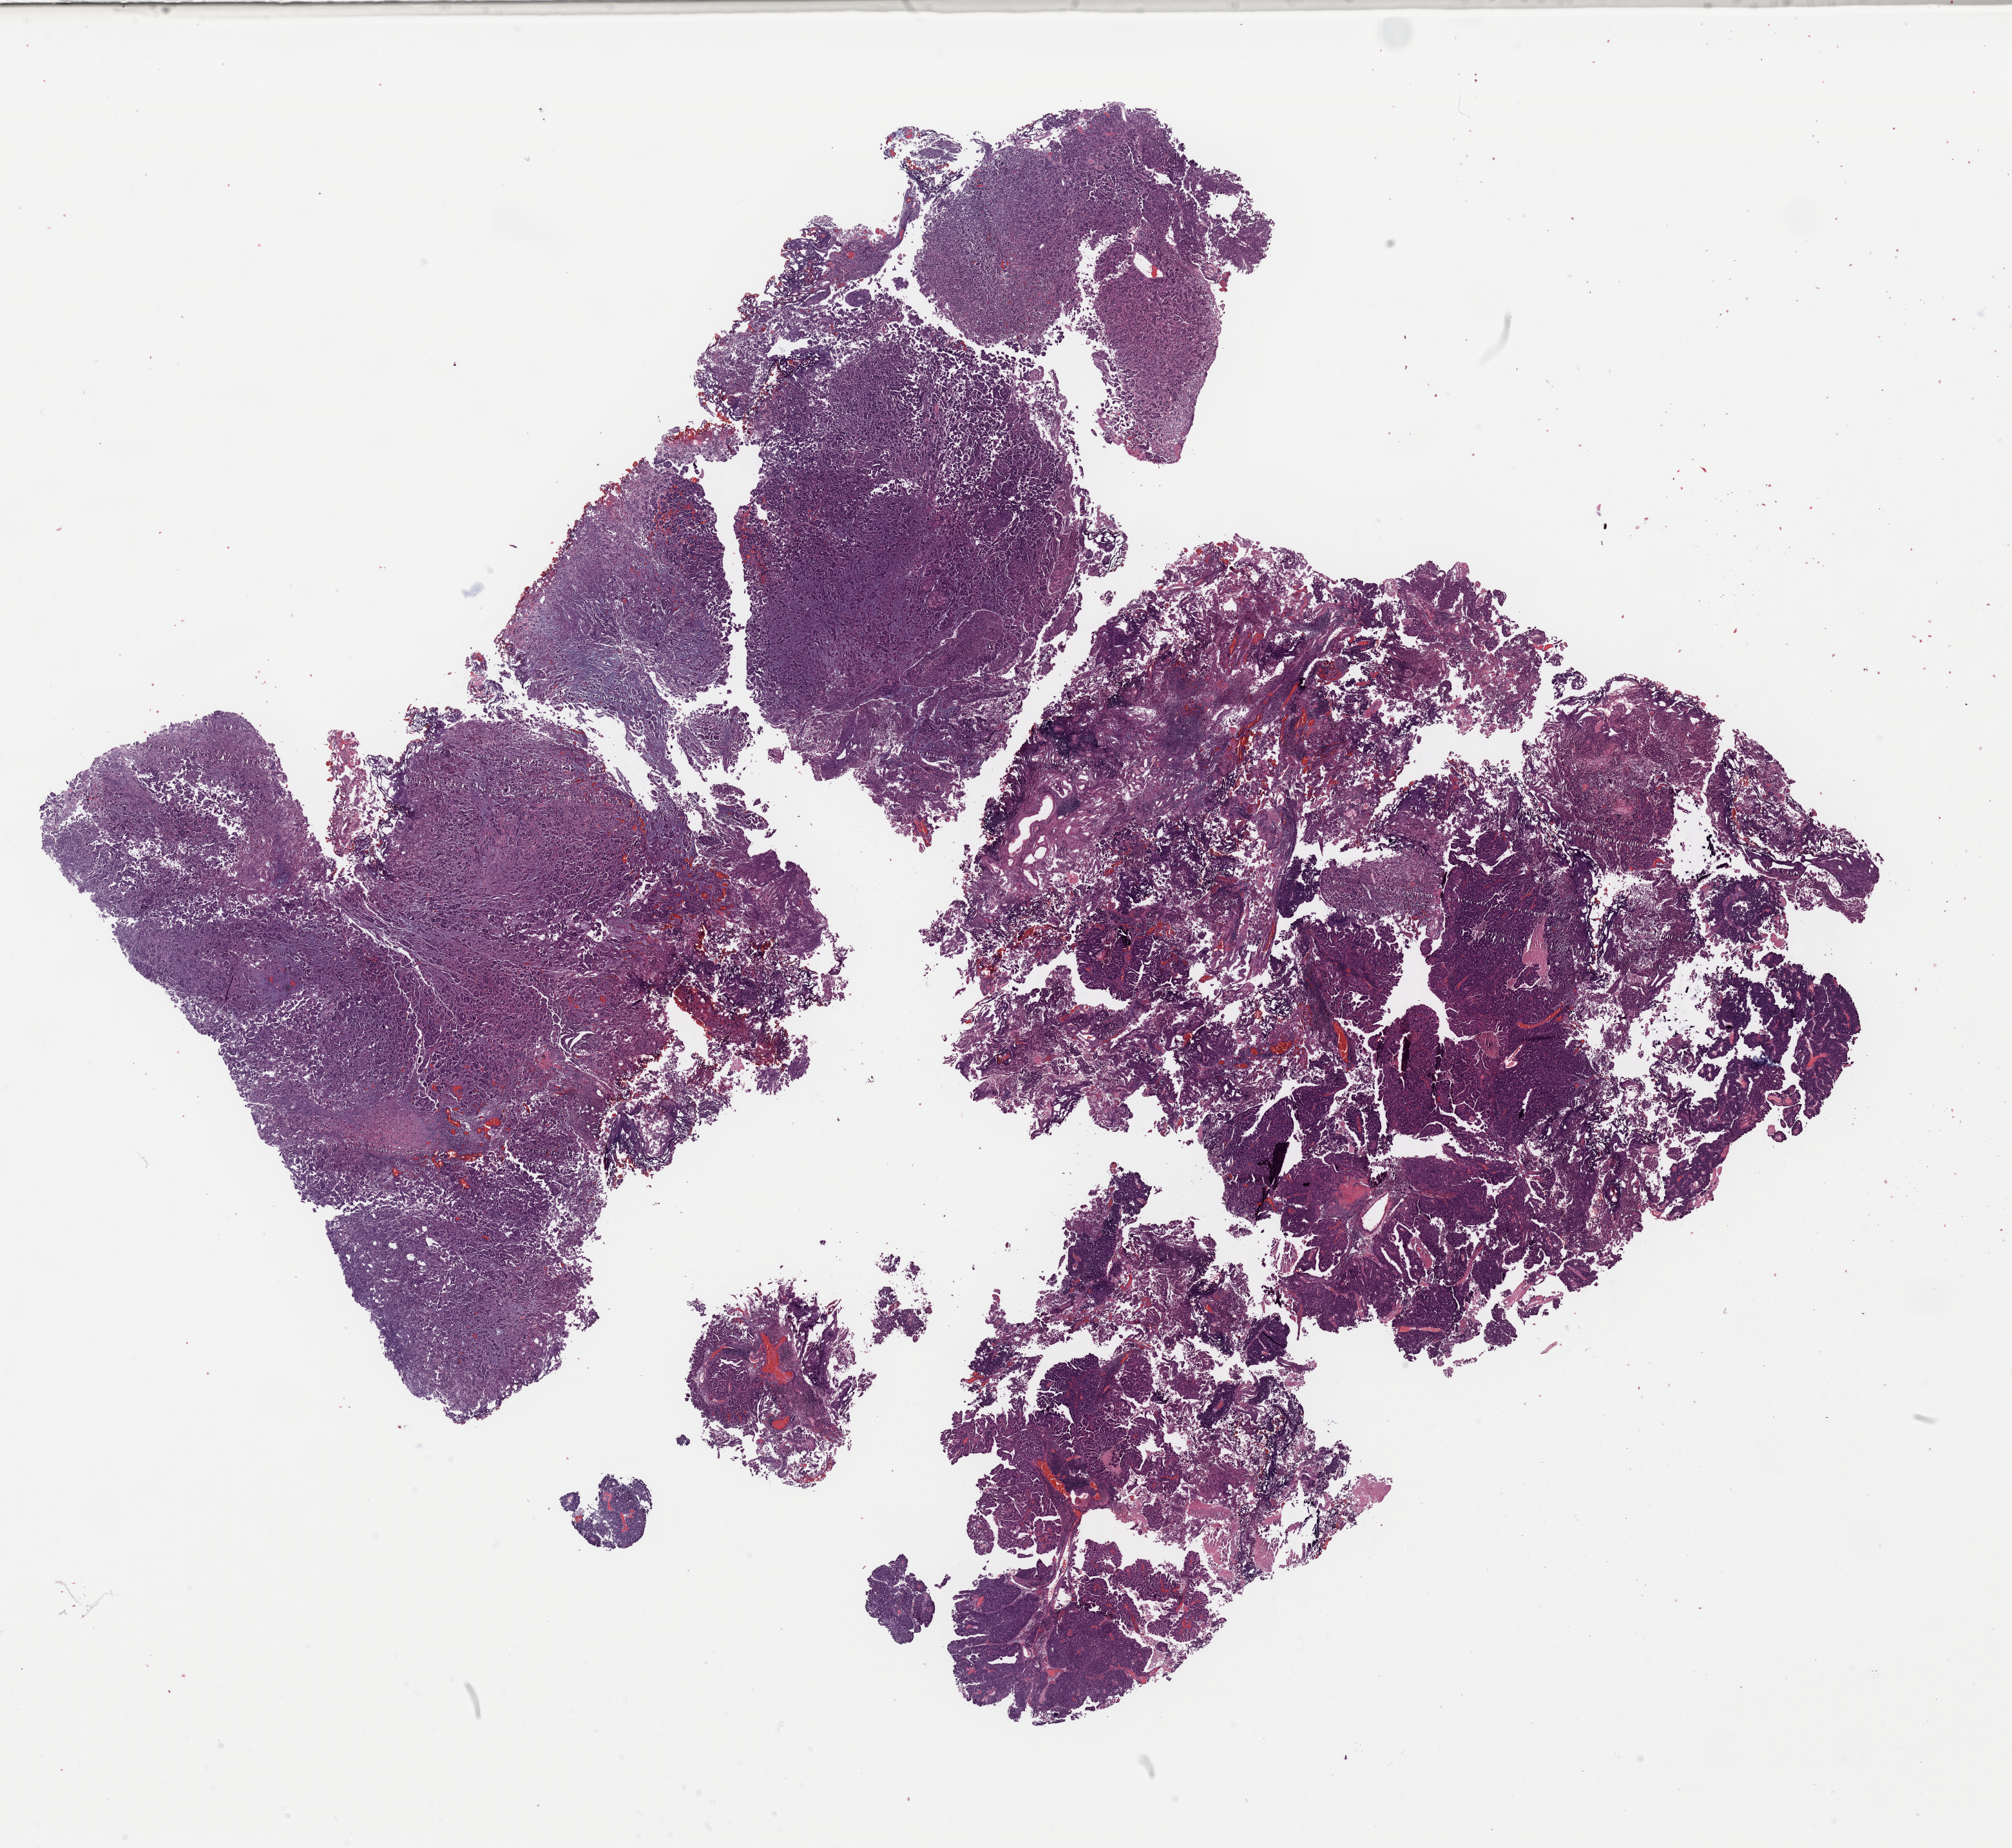
Whole-slide histology image, H&E, a low-resolution overview of the entire scanned area, about 24.7 x 22.7 mm (acquisition: 40x scan), formalin-fixed paraffin-embedded (FFPE) diagnostic section, bladder, primary tumour sample. Patient: male, age at initial diagnosis 56 years. Histologic grade: high grade.
Diagnosis: Transitional cell carcinoma. AJCC pathologic stage: II (7th edition).